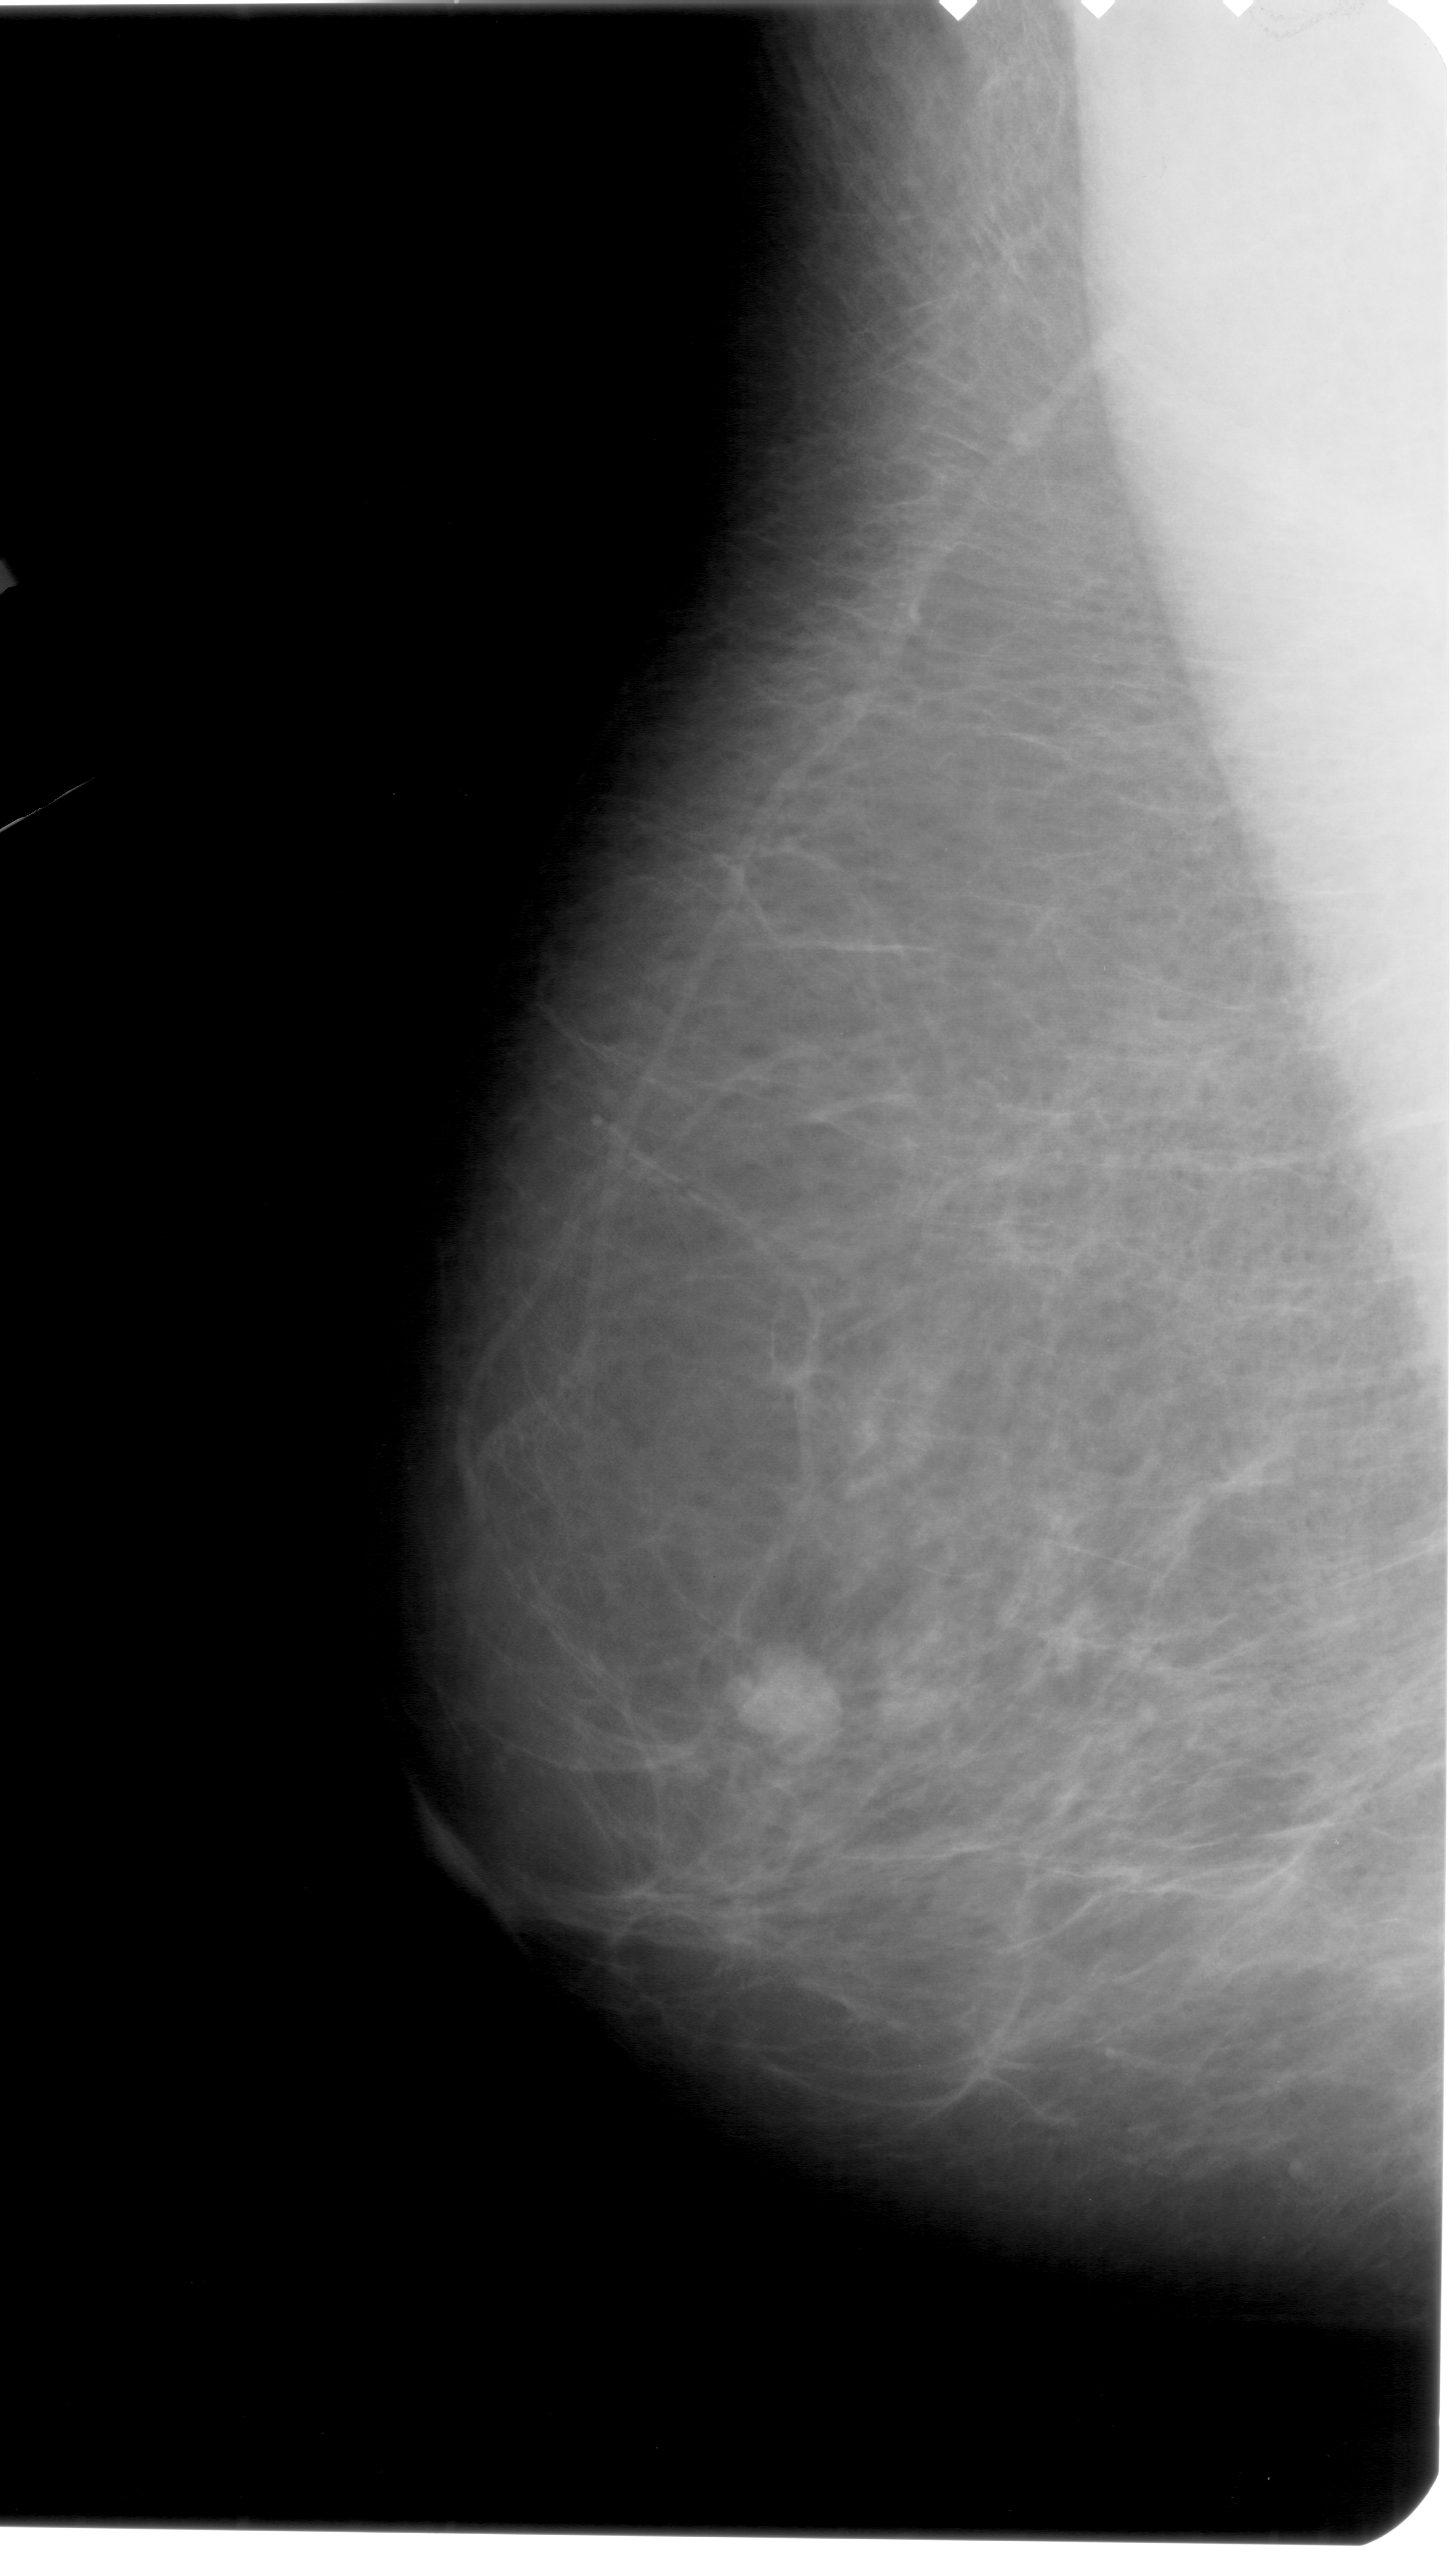
Scanned film-screen mammogram; left breast; mediolateral oblique (MLO) view; breast composition: heterogeneously dense (BI-RADS density category 3 of 4); 1456 × 2574 image matrix.
Marked abnormalities (boxes around the expert regions of interest):
- mass, shape lobulated, margins circumscribed; BI-RADS assessment category 4; pathology result (as recorded, not read from the image): malignant: bounding box <728,1644,847,1761> (left, top, right, bottom; pixels)